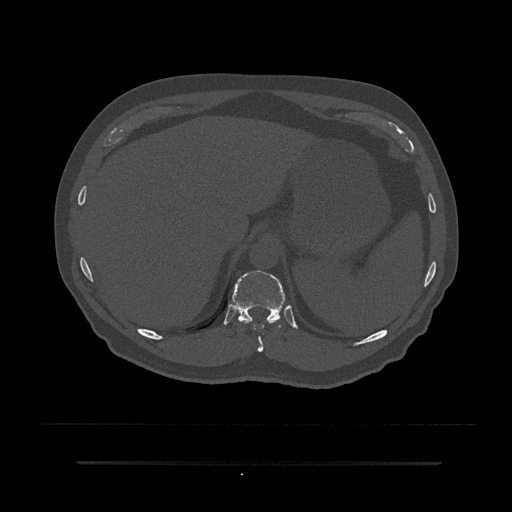
CT including the spine, one axial slice; position 292 of 797 along the scan axis; reconstruction kernel Br40s/3; 120 kVp; bone window (W 1800 / L 400 HU); 0.5 mm slice thickness; 512 × 512 image matrix, field of view 464 × 464 mm. Male patient, age 59 years. Case-level facts recorded for this patient, not image findings: primary cancer: bile ducts; vertebrae with lytic lesions (as recorded): T10.
Outlined on this slice (semi-automatic segmentation, software-assisted and operator-edited):
- T10 vertebra: bounding box <233,287,278,352> (left, top, right, bottom; pixels)
- T11 vertebra: <231,270,287,328>